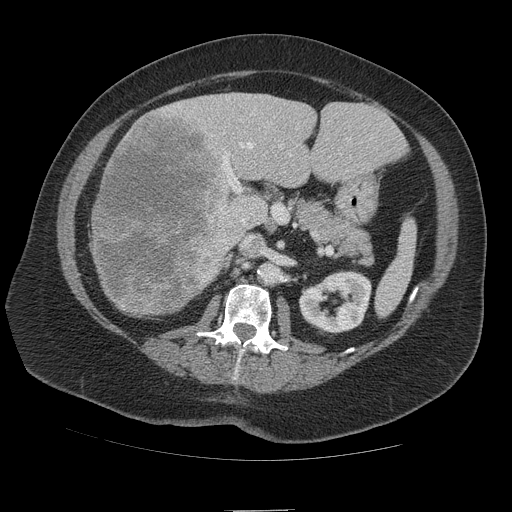
Contrast-enhanced abdominal CT (liver protocol), one axial slice. Slice 51 of 109 in the series (ordered by position). 140 kVp. Soft-tissue window (W 400 / L 40 HU). 2.5 mm slice thickness. 512 × 512 image matrix, field of view 420 × 420 mm. Case-level facts recorded for this patient, not image findings: diagnosis: hepatocellular carcinoma (patient treated with transarterial chemoembolisation; whether this scan precedes or follows treatment is not stated here); TNM stage (as recorded): Stage-IVB; Child-Pugh class: A.
Structures marked on this image (semi-automatic segmentation, software-assisted and operator-edited):
- liver parenchyma outside the tumour (the mass and vessels are separate outlines, so this box may not span the whole liver): bounding box [x1, y1, x2, y2] px = [92, 92, 406, 316]
- mass: [90, 106, 246, 316]
- liver vessels: [222, 142, 292, 224]